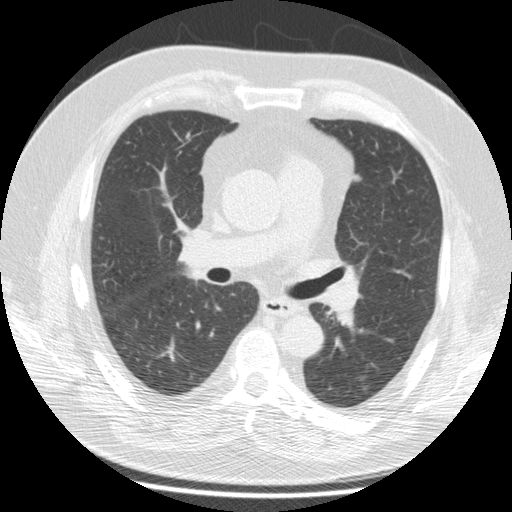
Chest CT (low-dose screening protocol), one axial image. Third annual screen. Lung window (W 1500 / L -600 HU). Standard (soft-tissue) reconstruction kernel (STANDARD). 120 kVp. Slice 73 of 172 in the series. 512 × 512 image matrix, field of view 364 × 364 mm. Male, age 69 years at enrolment. Former smoker at enrolment.
- Expert-annotated lung lesion, bounding box <354,371,381,403> (left, top, right, bottom; pixels).
- The screening reader recorded 2 non-calcified nodules or masses ≥4 mm on this exam (left lower lobe, left lower lobe); which of them this box marks is not recorded.
- Official screen result: positive, other.
- Participant outcome: lung cancer diagnosed 224 days after this screen — squamous cell carcinoma, NOS, left lower lobe, moderately differentiated (G2), stage IA (AJCC 6th edition), 14 mm at pathology.